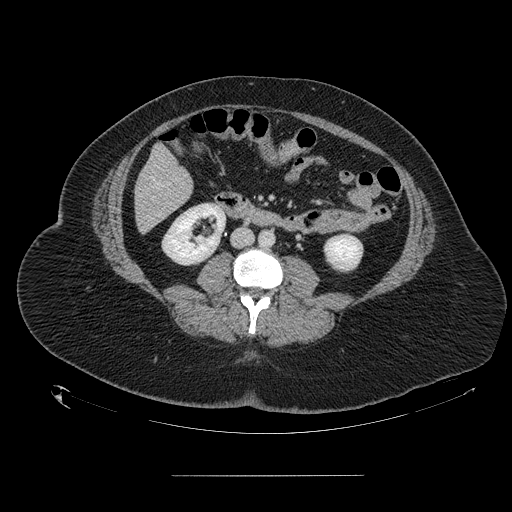
Contrast-enhanced abdominal CT, one axial slice. Position 36 of 164 along the scan axis. 120 kVp. Intravenous contrast given. Soft-tissue window (W 400 / L 40 HU). 2.5 mm slice thickness. 512 × 512 image matrix, field of view 495 × 495 mm. Female patient, age 52 years. Case-level facts recorded for this patient, not image findings: diagnosis: colorectal cancer liver metastases, imaged before liver resection; multiple liver metastases: yes; largest metastasis: 3.5 cm; disease in both lobes: no.
Structures marked on this image (outlined manually by an expert reader):
- hepatic veins: bounding box [x1, y1, x2, y2] px = [152, 178, 161, 186]
- liver: [135, 147, 193, 231]